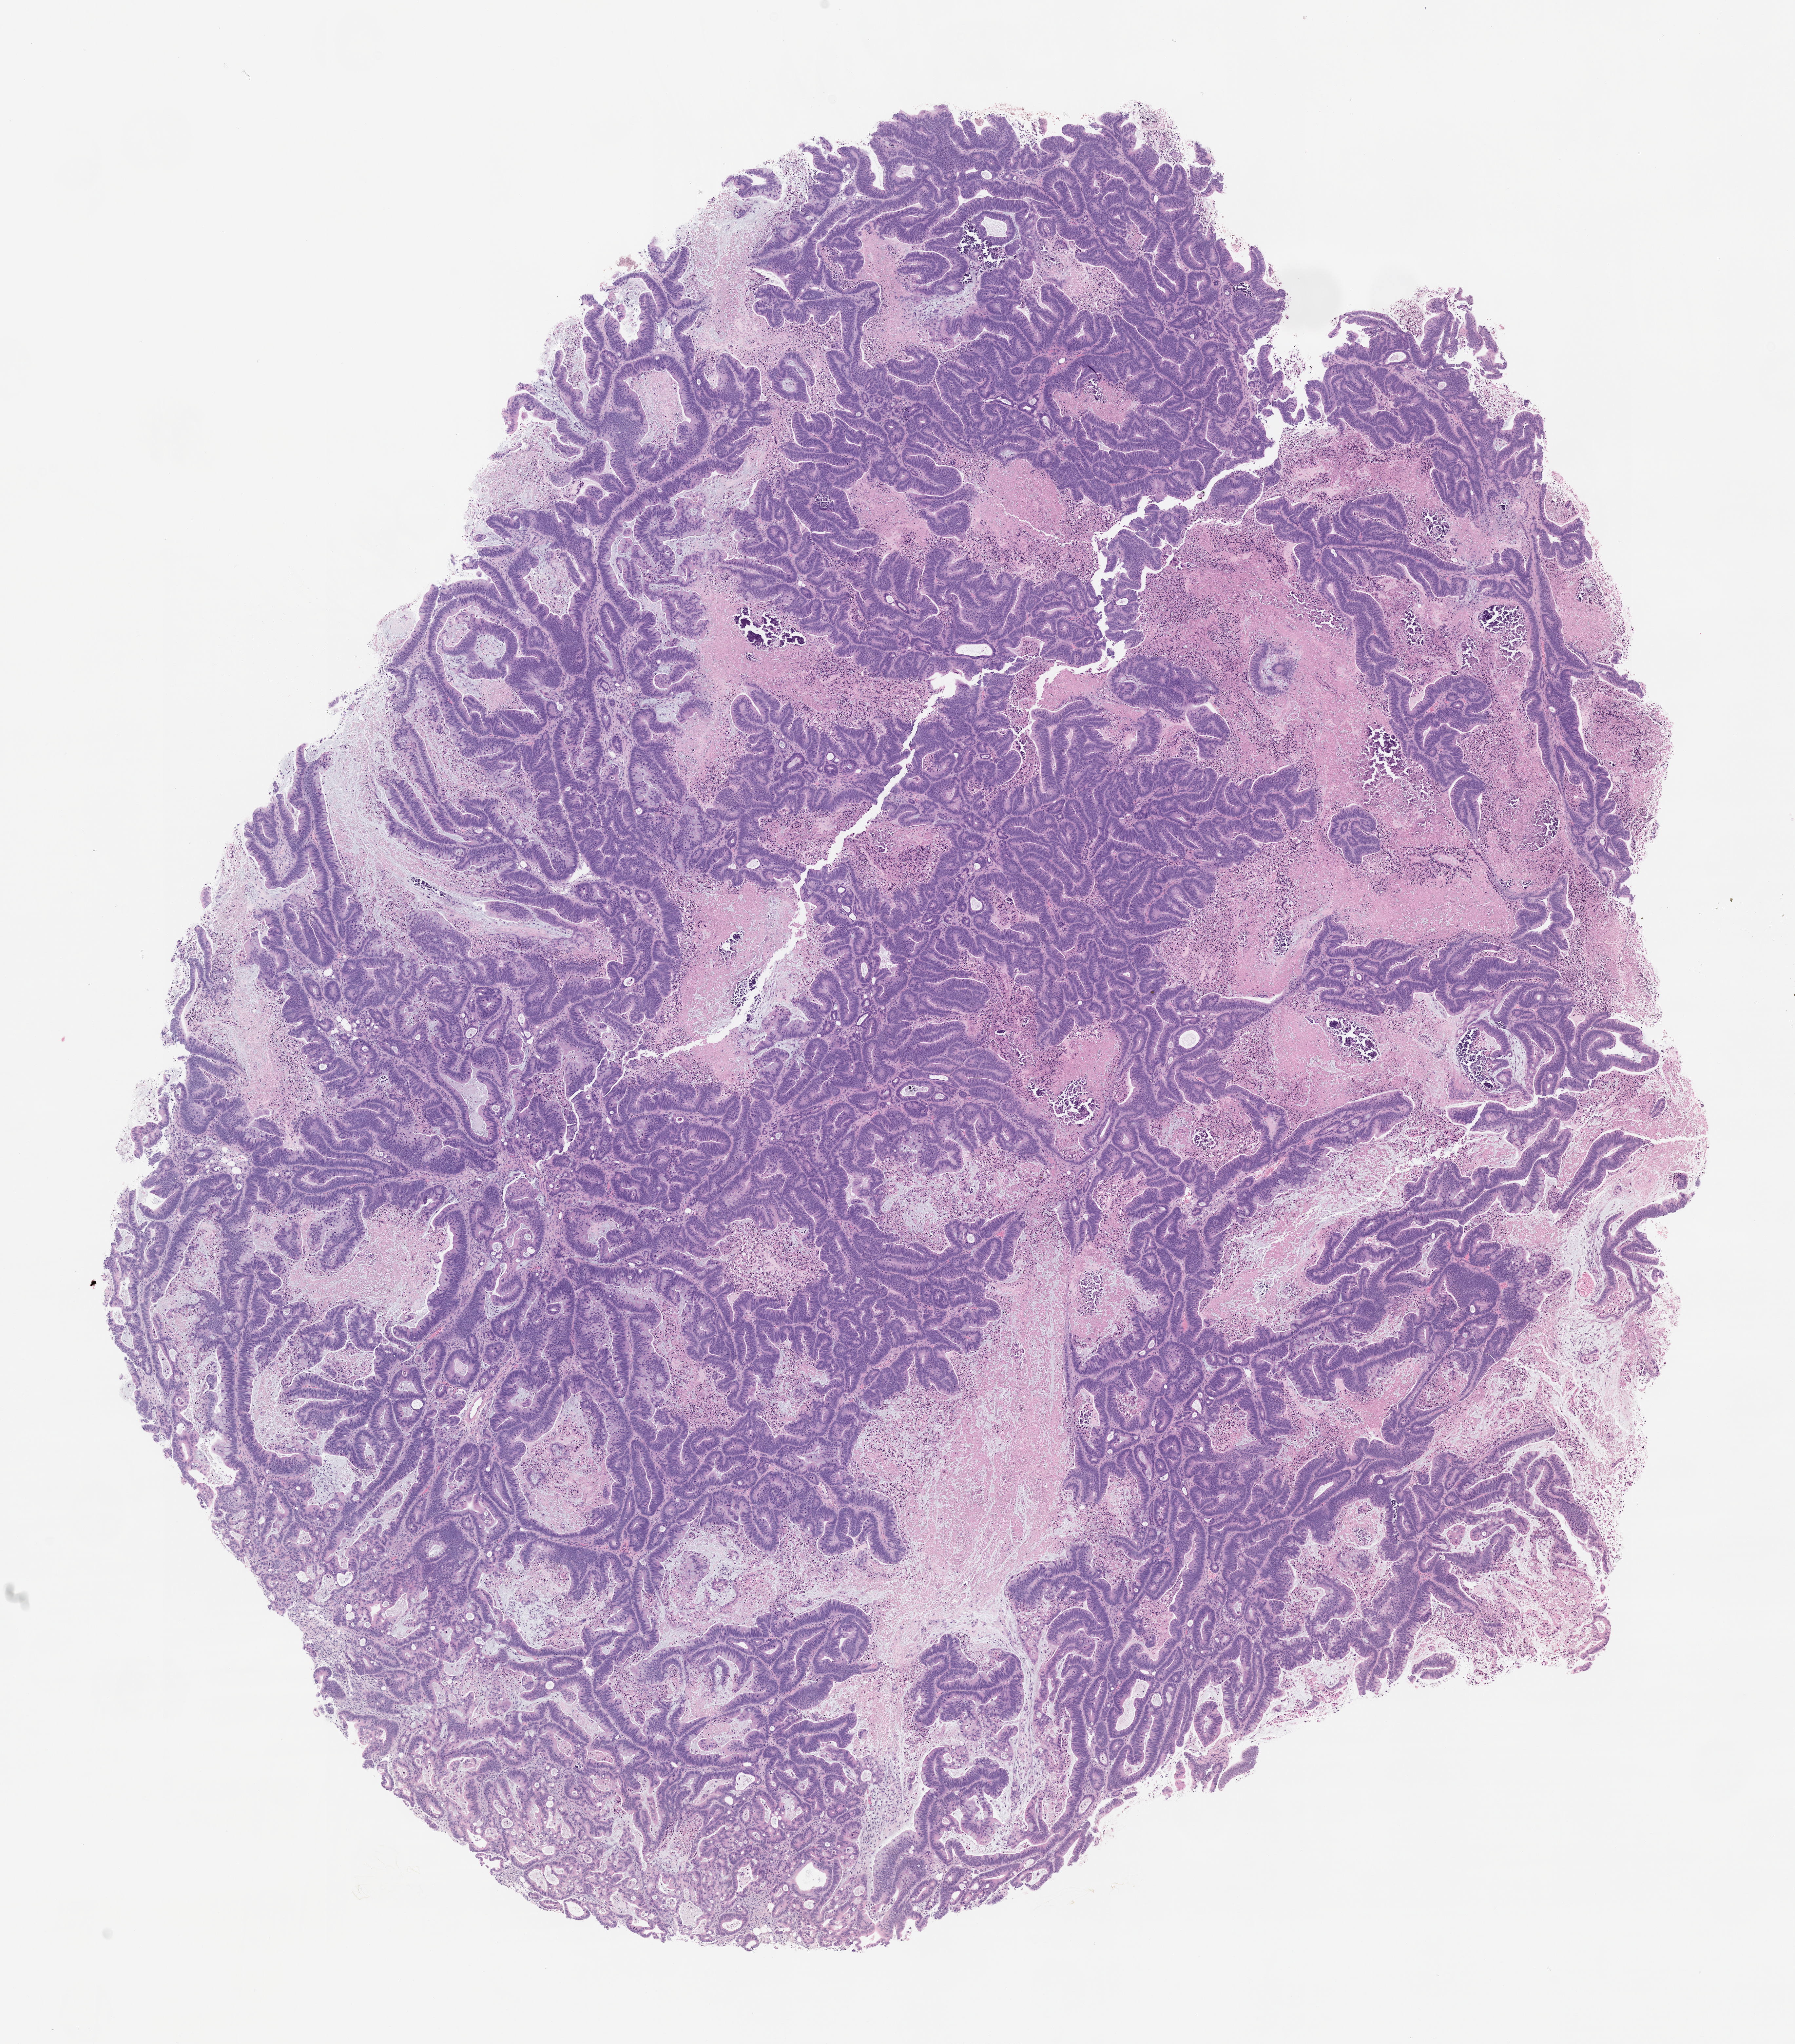
Hematoxylin and eosin (H&E) whole-slide image of a patient-derived xenograft (PDX) tumor grown in a mouse, passage 1, whole scanned area (about 11.0 x 12.5 mm) shown as a low-resolution overview; FFPE section; tumor site category: colon.
Originating patient diagnosis: Colon Adenocarcinoma.